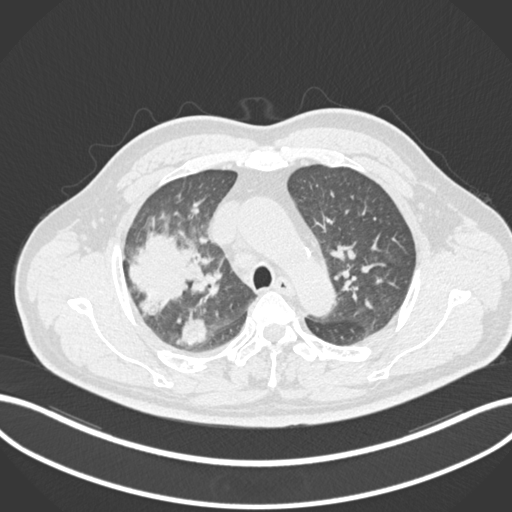
Chest CT, one axial slice; slice 667 of 852 in the series (ordered by position); 120 kVp; lung window (W 1500 / L -600 HU); 1 mm slice thickness; 512 × 512 image matrix, field of view 400 × 400 mm. Male patient, age 55 years. From the clinical record (not read from this slice): clinical TNM (as recorded): T3 N2 M1.
Outlined on this slice (rectangle marked by the reading radiologist):
- lung tumour (recorded histology: adenocarcinoma): bounding box (x1, y1, x2, y2) in pixels: (126, 229, 203, 316)